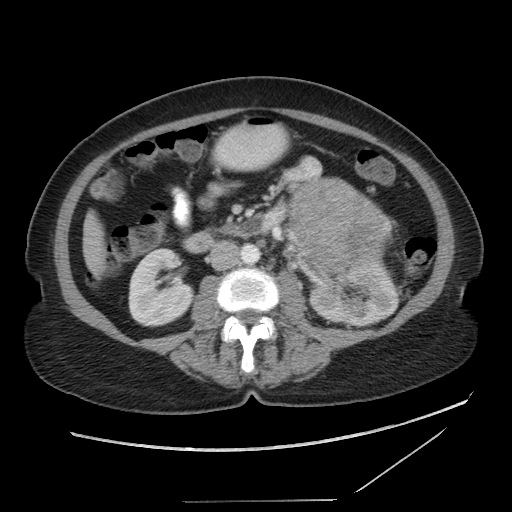
Contrast-enhanced abdominal CT, one axial slice. Position 44 of 86 along the scan axis. 120 kVp. Intravenous contrast given. Soft-tissue window (W 400 / L 40 HU). 5 mm slice thickness. 512 × 512 image matrix. Female patient, age 77 years. From the clinical record (not read from this slice): diagnosis: adrenocortical carcinoma; tumour side: left adrenal; tumour size at pathology: 13.1 cm; Ki-67 index: 10 %; stage (as recorded): 3.
Annotated regions visible in this slice (semi-automatically segmented with operator editing):
- mass: bounding box <291,180,390,279> (left, top, right, bottom; pixels)